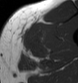
MRI of an extremity soft-tissue mass, one axial slice; position 30 of 43 along the scan axis; MR volume resampled by the dataset authors to the PET/CT grid (not the native acquisition matrix); 3.27 mm slice thickness; 78 × 83 image matrix, field of view 76 × 81 mm. Male patient. From the clinical record (not read from this slice): histological type: pleiomorphic leiomyosarcoma; grade: high; site of the primary tumour: left thigh.
Outlined on this slice (expert contour drawn on MRI and transferred to this co-registered scan by the dataset authors):
- gross tumour volume including surrounding oedema: bounding box (x1, y1, x2, y2) in pixels: (20, 24, 44, 59)
- gross tumour volume (mass): (25, 40, 41, 57)